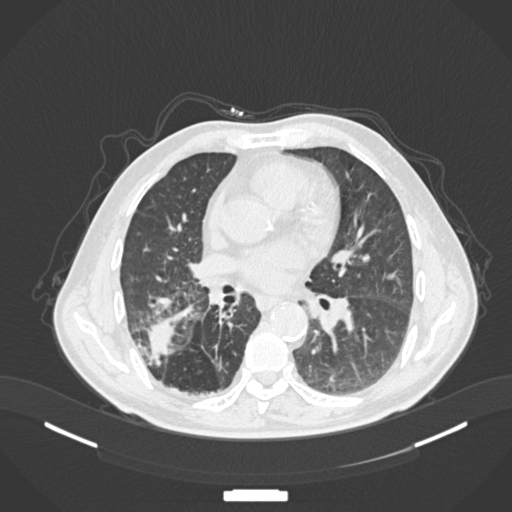
Chest CT, one axial slice. Slice 79 of 201 in the series (ordered by position). Reconstruction kernel B30f. 120 kVp. Lung window (W 1500 / L -600 HU). 1 mm slice thickness. 512 × 512 image matrix, field of view 400 × 400 mm. Patient: male, 72 years. From the clinical record (not read from this slice): clinical TNM (as recorded): T3 N2 M0.
Structures marked on this image (rectangle marked by the reading radiologist):
- lung tumour (recorded histology: adenocarcinoma): box from (x=145, y=317) to (x=174, y=367) px